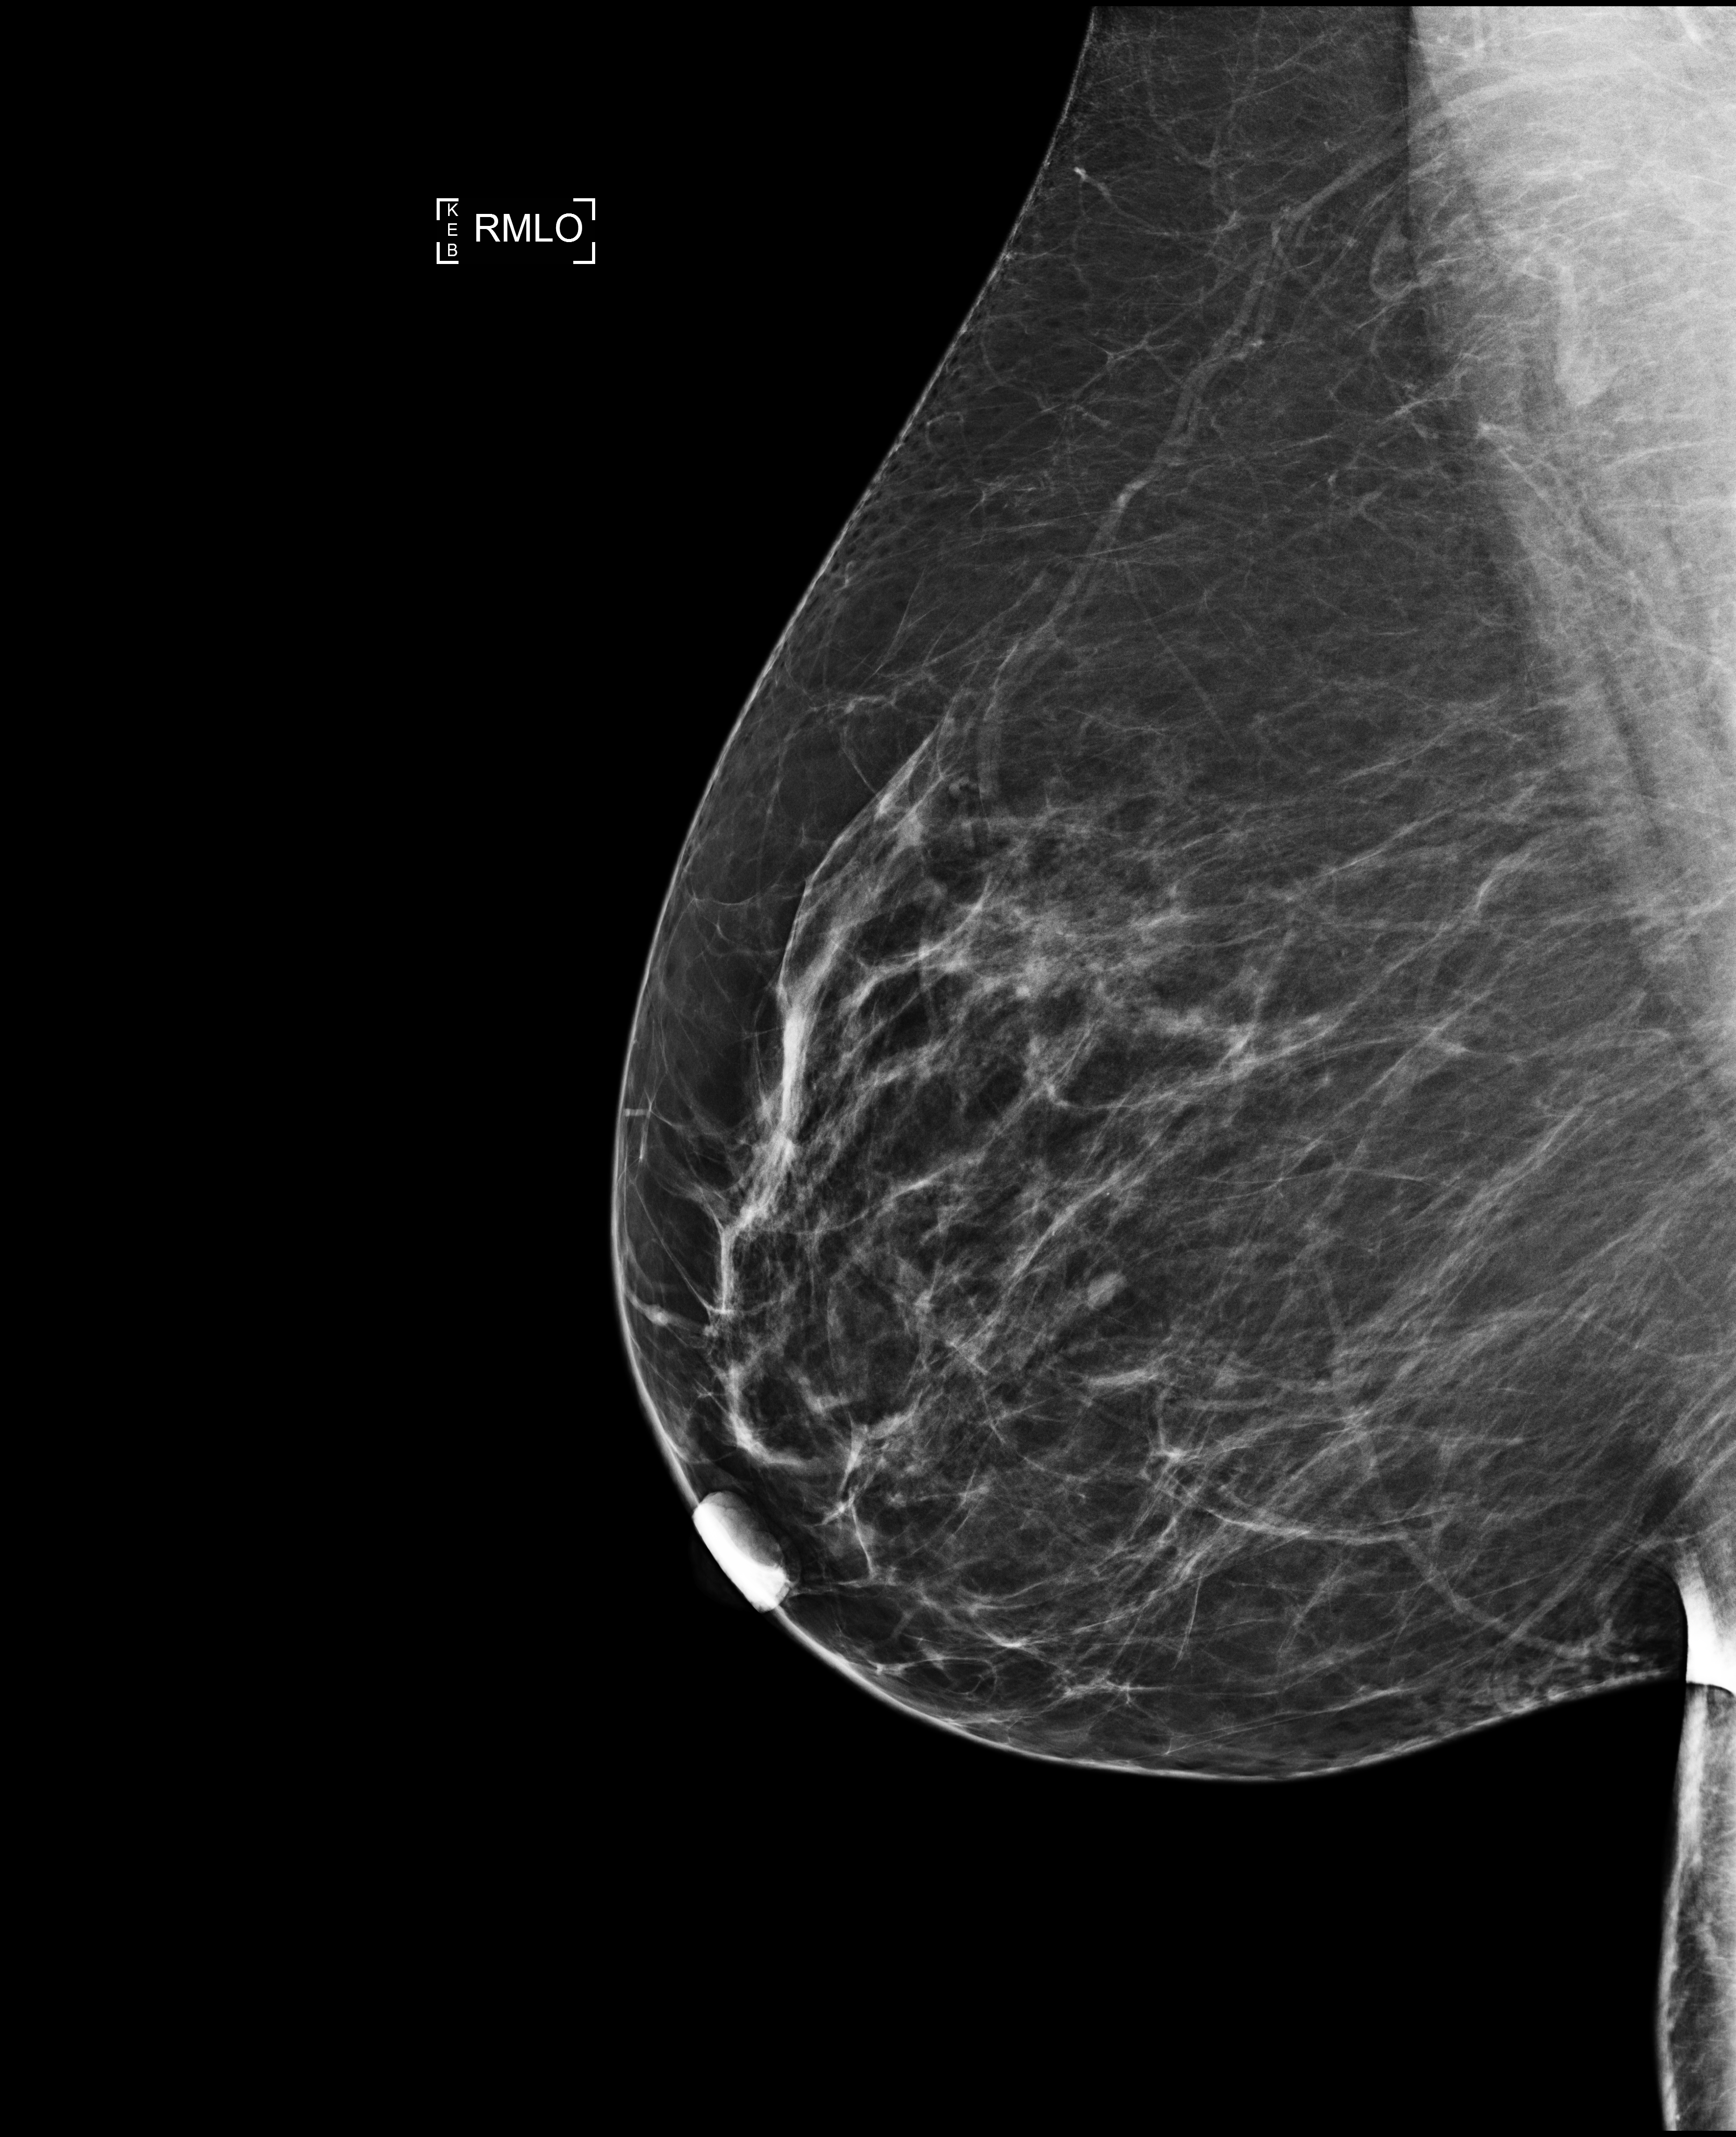
Screening examination, system: Selenia Dimensions. Patient aged 53 years (female).
Image type: full-field digital mammogram. Breast: right. Projection: mediolateral oblique (MLO) view.